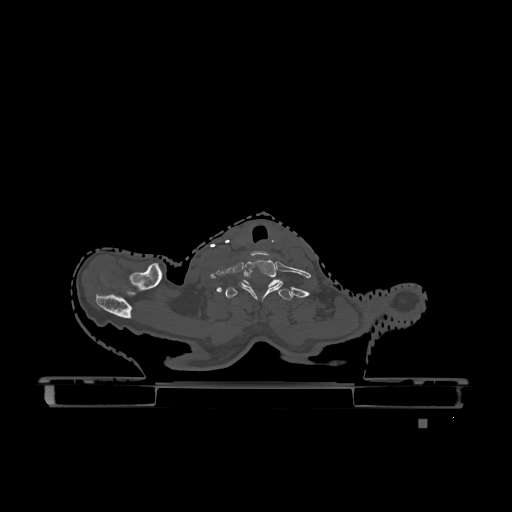
CT including the spine, one axial slice. Position 1019 of 1317 along the scan axis. Bone window (W 1800 / L 400 HU). 0.5 mm slice thickness. 512 × 512 image matrix. Patient: female, 74 years. Case-level facts recorded for this patient, not image findings: primary cancer: lung.
Structures marked on this image (semi-automatic segmentation, software-assisted and operator-edited):
- T1 vertebra: box from (x=225, y=280) to (x=293, y=300) px